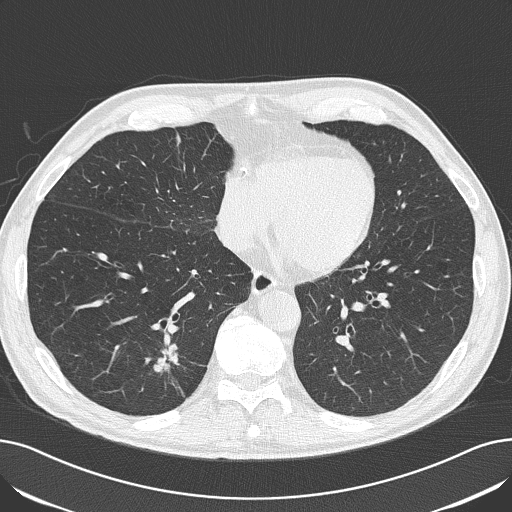
Low-dose screening chest CT, axial slice; baseline annual screen; lung window (W 1500 / L -600 HU); 2 mm slice thickness; slice 121 of 182 in the series. Male participant, aged 71 years at enrolment. Current smoker at enrolment.
Lesion marked by an expert reader, bounding box (x1, y1, x2, y2) in pixels: (135, 329, 197, 389). The exam's reader record, not a measurement of the box and not confirmed to be the same lesion: non-calcified nodule or mass ≥4 mm, right lower lobe, 14 × 14 mm, spiculated (stellate) margins, soft tissue attenuation. Official screen result: positive, change unspecified: nodule(s) >= 4 mm or enlarging nodule(s), mass(es), or other non-specific abnormalities suspicious for lung cancer. Later outcome: lung cancer diagnosed 145 days after this screen — adenocarcinoma, NOS, right lower lobe, moderately differentiated (G2), stage IA (AJCC 6th edition), 24 mm at pathology.